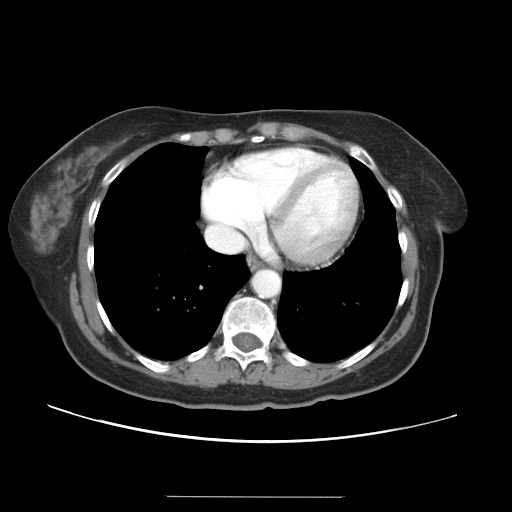
Contrast-enhanced abdominal CT, one axial slice; position 34 of 34 along the scan axis; reconstruction kernel STANDARD; intravenous contrast given; soft-tissue window (W 400 / L 40 HU); 5 mm slice thickness; 512 × 512 image matrix. Female patient, age 69 years. Case-level facts recorded for this patient, not image findings: diagnosis: colorectal cancer liver metastases, imaged before liver resection; multiple liver metastases: yes; largest metastasis: 1.4 cm; chemotherapy before resection: no.
Outlined on this slice (manually delineated by an expert):
- hepatic veins: bounding box [x1, y1, x2, y2] px = [207, 150, 325, 253]